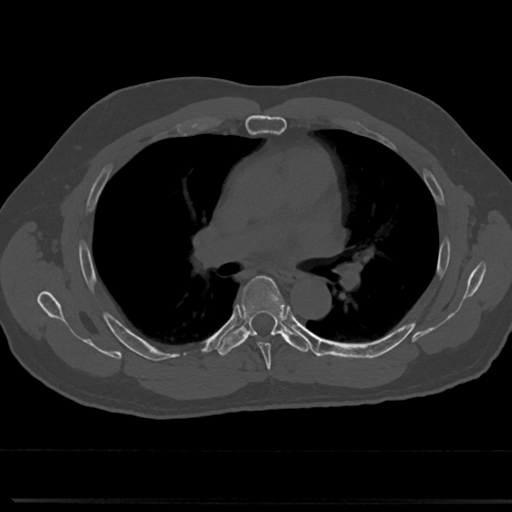
CT including the spine, one axial slice; position 471 of 817 along the scan axis; reconstruction kernel Br40s/3; 120 kVp; bone window (W 1800 / L 400 HU); 0.5 mm slice thickness; 512 × 512 image matrix, field of view 355 × 355 mm. Patient: male, 61 years. Case-level facts recorded for this patient, not image findings: primary cancer: prostate.
Structures marked on this image (semi-automatic segmentation, software-assisted and operator-edited):
- T5 vertebra: bounding box <241,277,287,361> (left, top, right, bottom; pixels)
- T6 vertebra: <220,276,286,353>